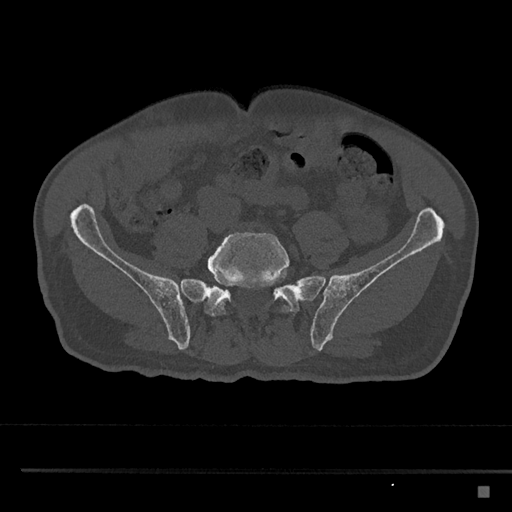
CT including the spine, one axial slice; position 561 of 797 along the scan axis; 120 kVp; bone window (W 1800 / L 400 HU); 512 × 512 image matrix, field of view 391 × 391 mm. Patient: male, 59 years. Case-level facts recorded for this patient, not image findings: primary cancer: prostate.
Outlined on this slice (semi-automatically segmented with operator editing):
- L5 vertebra: bounding box <207,232,292,316> (left, top, right, bottom; pixels)